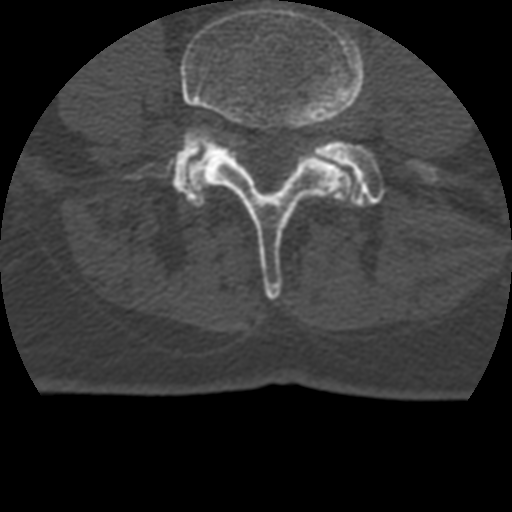
CT including the spine, one axial slice. Slice 60 of 399 in the series (ordered by position). Reconstruction kernel STANDARD. 120 kVp. Bone window (W 1800 / L 400 HU). 512 × 512 image matrix. Patient age 69 years. From the clinical record (not read from this slice): primary cancer: prostate.
Structures marked on this image (semi-automatic segmentation, software-assisted and operator-edited):
- L4 vertebra: bounding box <138,8,365,300> (left, top, right, bottom; pixels)
- L5 vertebra: <172,135,432,206>